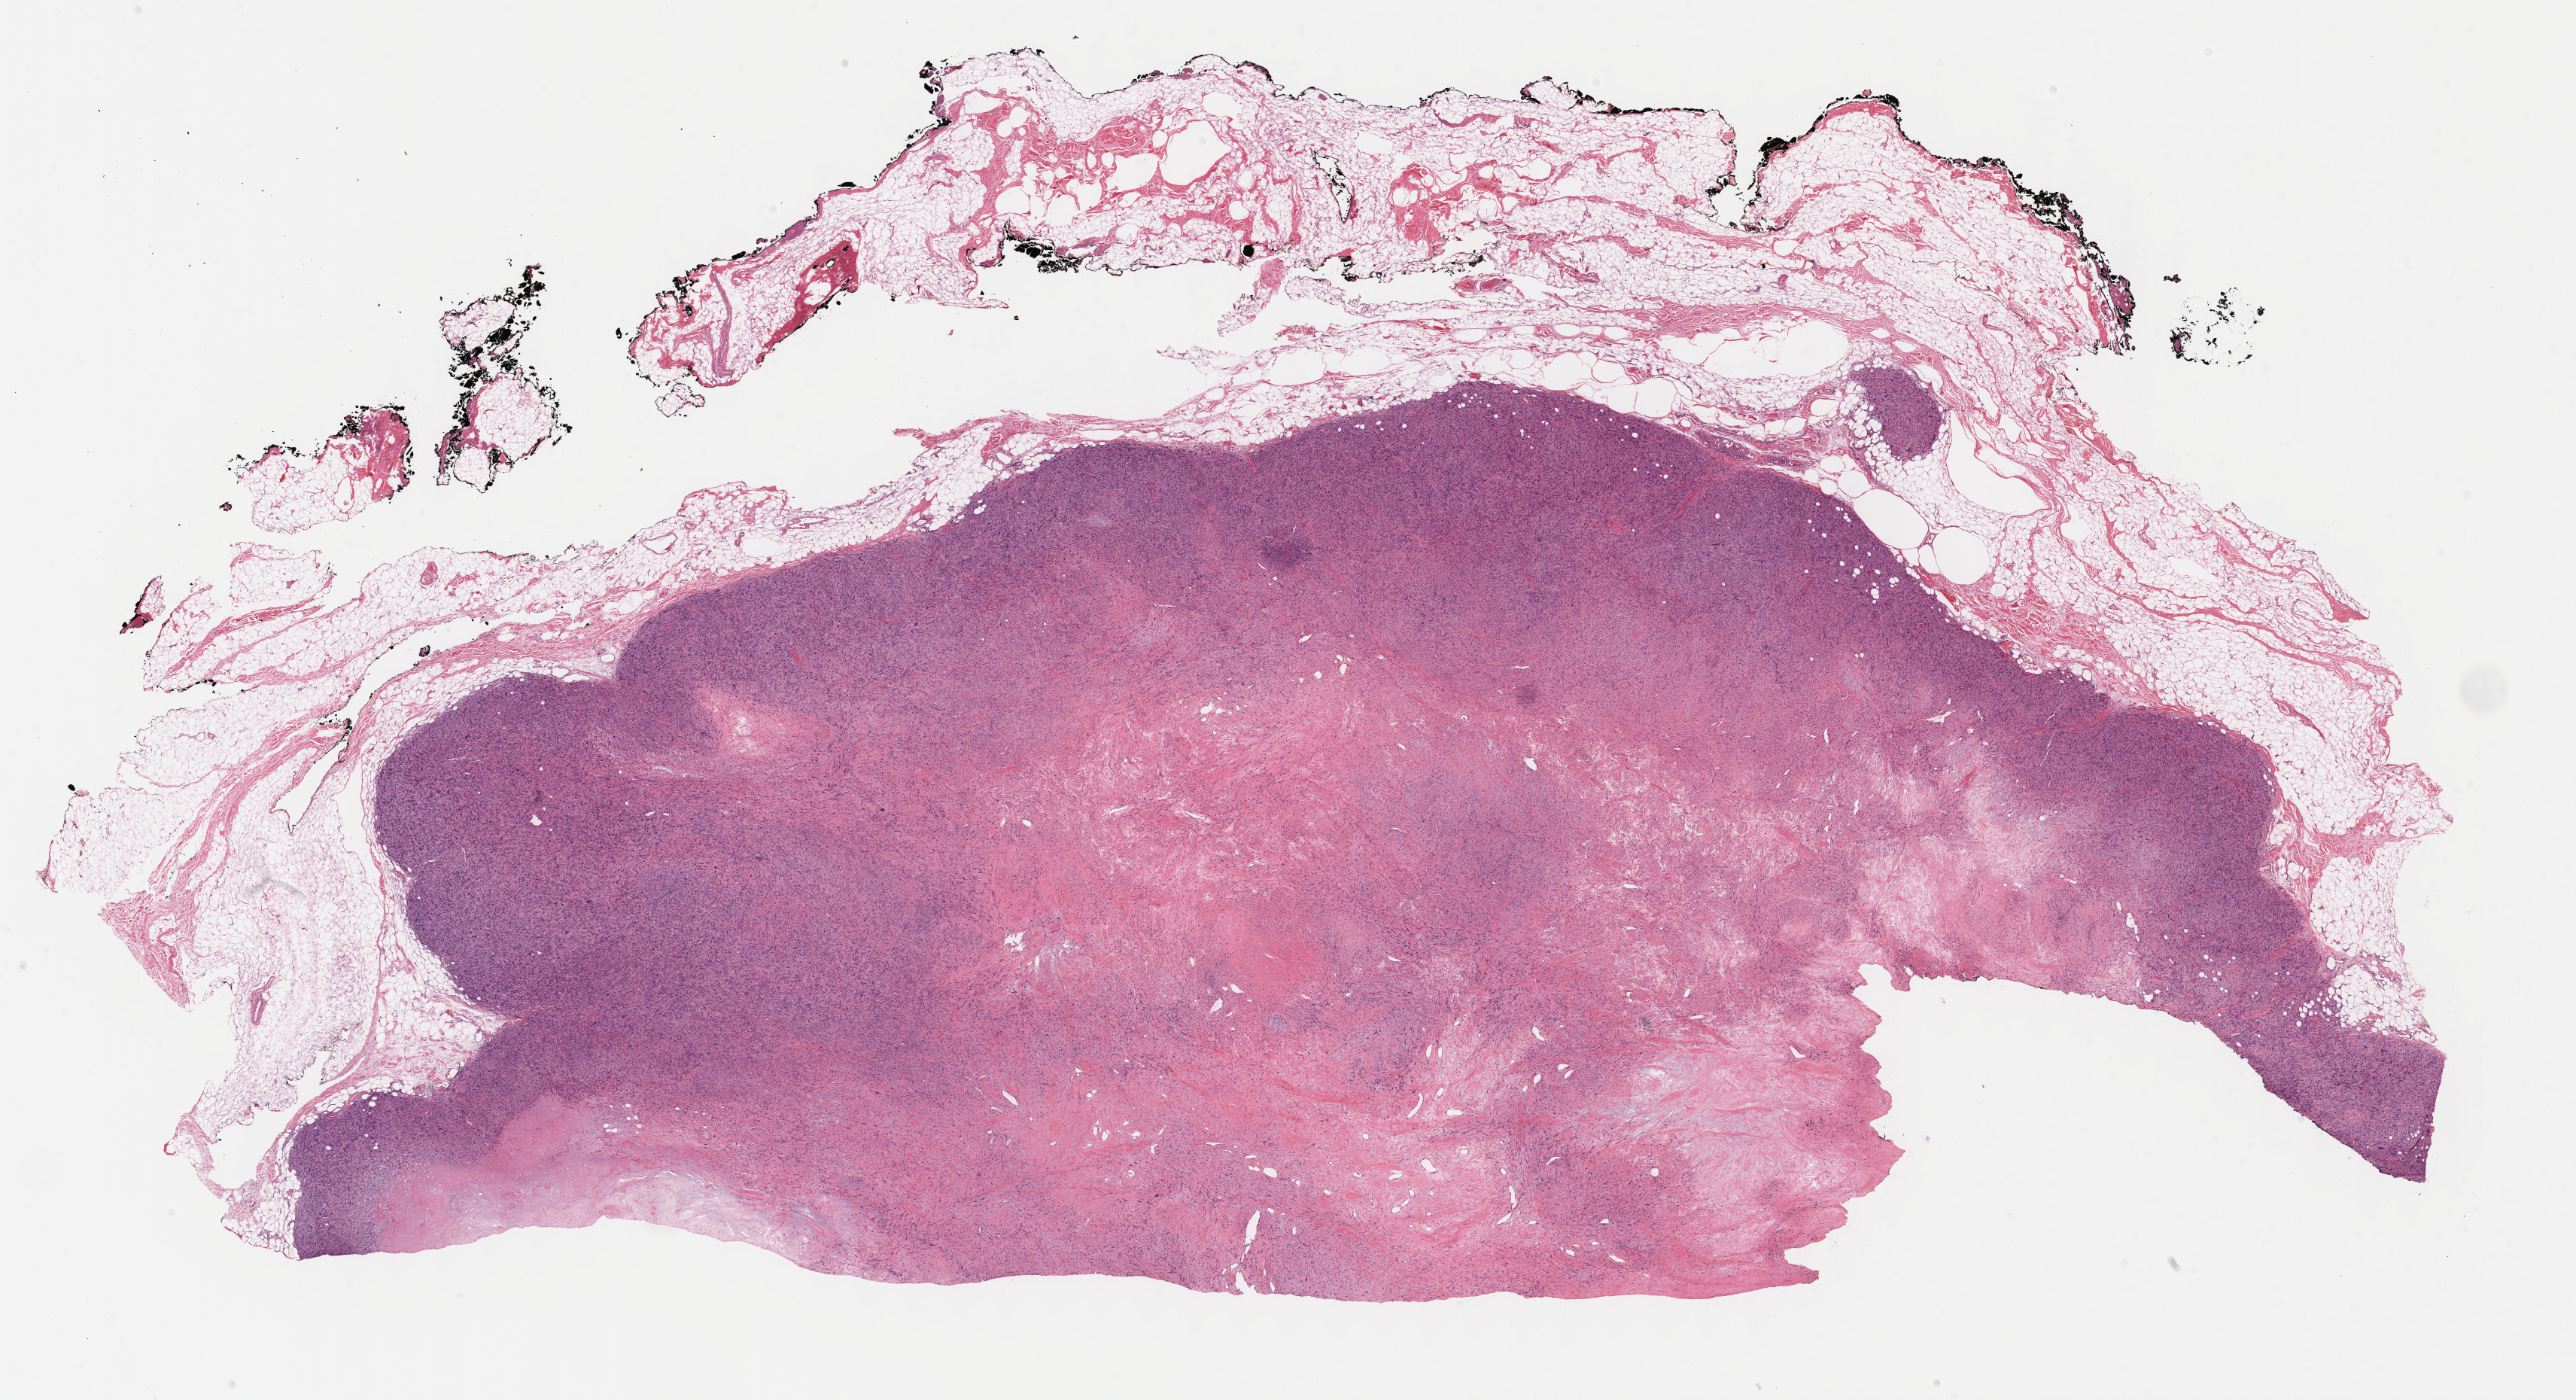
Whole-slide histology image, H&E, whole scanned area (about 27.7 x 15.0 mm, slide scanned at 40x) shown as a low-resolution overview. Formalin-fixed paraffin-embedded (FFPE) diagnostic section. Primary tumour sample from the connective, subcutaneous and other soft tissues. Female, age 52 years at initial diagnosis.
- pathologic diagnosis: Leiomyosarcoma, NOS (connective, subcutaneous and other soft tissues of upper limb and shoulder)